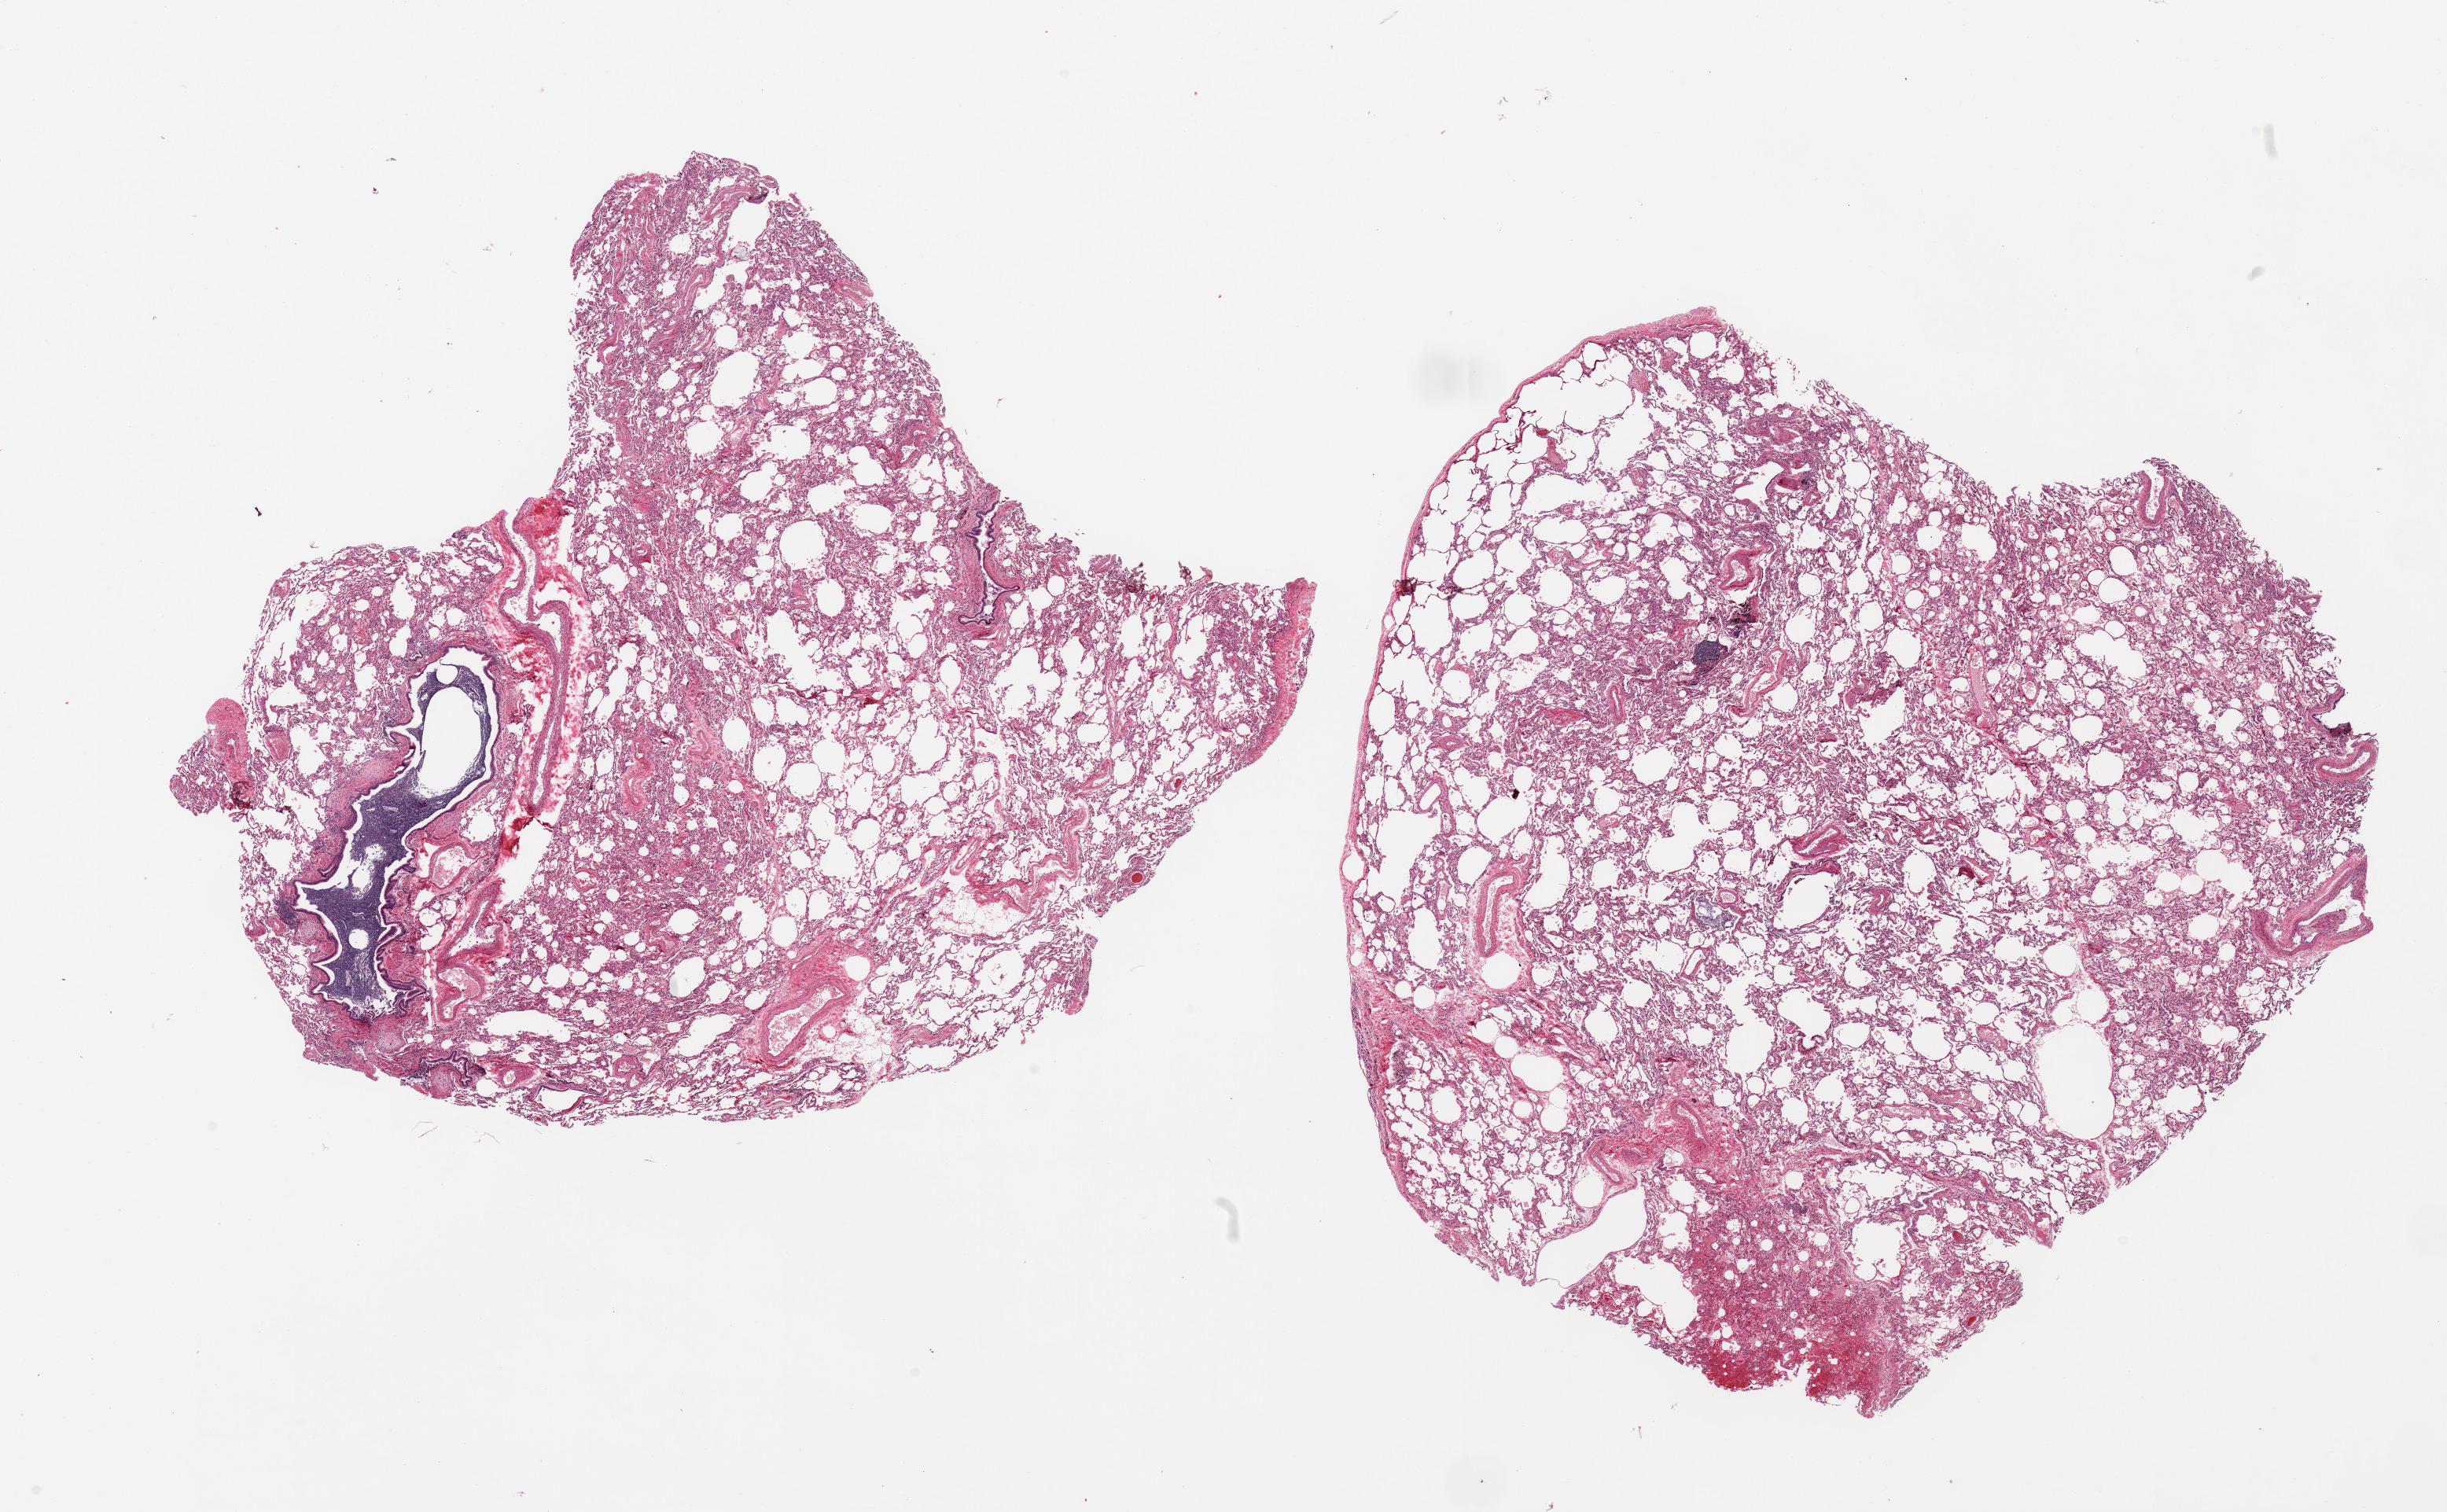
Digitized hematoxylin and eosin (H&E)-stained section, whole scanned area (about 24.6 x 15.2 mm, slide scanned at 20x) shown as a low-resolution overview, PAXgene-fixed, paraffin-embedded tissue, target tissue: lung, donor tissue sample. Donor sex: male.
Reviewer comment on this tissue sample: 2 pieces, mild congestion/ prominent intrabronchial fibrinopurulent aggregates.